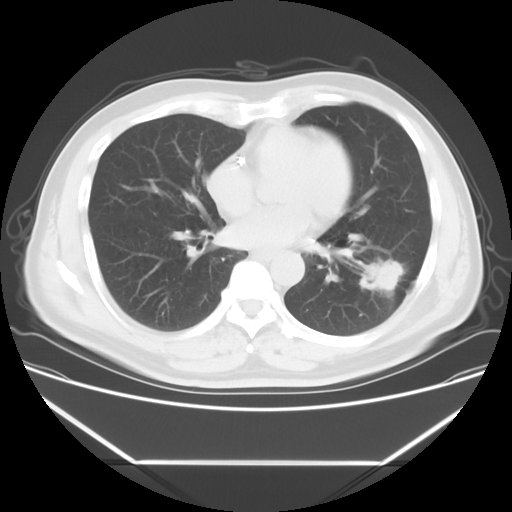
Chest CT, one axial slice; position 26 of 57 along the scan axis; reconstruction kernel STANDARD; lung window (W 1500 / L -600 HU); 5 mm slice thickness; 512 × 512 image matrix. Male patient, age 53 years. Case-level facts recorded for this patient, not image findings: clinical TNM (as recorded): T1c N0 M0.
Outlined on this slice (bounding box drawn by a radiologist):
- lung tumour (recorded histology: adenocarcinoma): bounding box <359,245,408,308> (left, top, right, bottom; pixels)